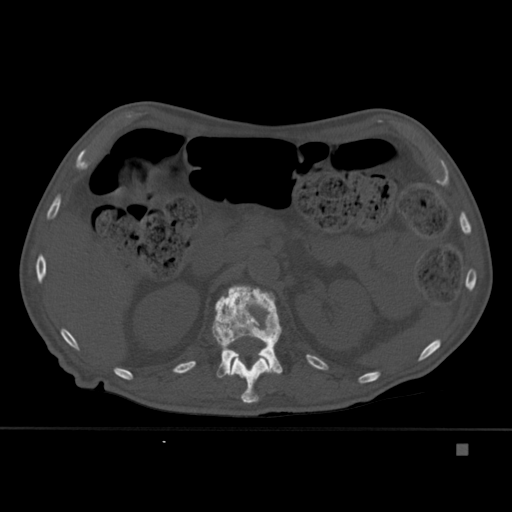
CT including the spine, one axial slice; position 190 of 451 along the scan axis; bone window (W 1800 / L 400 HU); 1.5 mm slice thickness; 512 × 512 image matrix, field of view 378 × 378 mm. Patient: male, 75 years. From the clinical record (not read from this slice): primary cancer: prostate.
Structures marked on this image (semi-automatic segmentation, software-assisted and operator-edited):
- L1 vertebra: bounding box (x1, y1, x2, y2) in pixels: (212, 285, 283, 378)
- T12 vertebra: (230, 355, 271, 404)